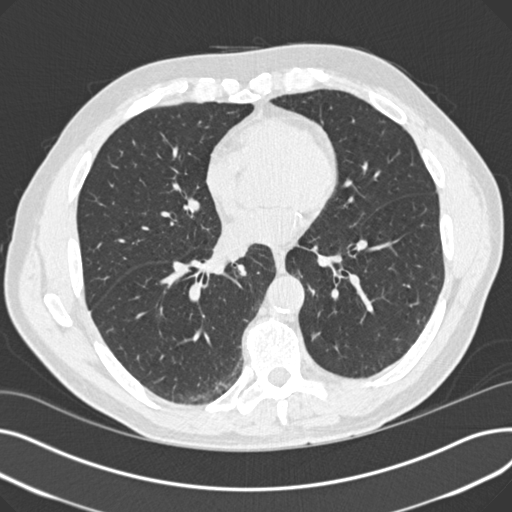
Low-dose screening chest CT, axial slice; second annual screen; lung window (W 1500 / L -600 HU); 2 mm slice thickness; standard (soft-tissue) reconstruction kernel (B30f); slice 96 of 163 in the series. Male, age 64 years at enrolment. Former smoker at enrolment.
Expert-annotated lung lesion, bounding box [x1, y1, x2, y2] px = [299, 317, 338, 362]. Screening reader's record for this exam (one nodule recorded; not confirmed to be the boxed lesion): non-calcified nodule or mass ≥4 mm, left lower lobe, 6 × 5 mm, smooth margins, ground glass attenuation, pre-existing on the prior screen: yes; interval growth: no. Official screen result: positive, no significant change: stable abnormalities potentially related to lung cancer, unchanged since the prior screening exam. Lung cancer was diagnosed 417 days after this screen: adenocarcinoma with mixed subtypes, left lower lobe, well differentiated (G1), stage IA (AJCC 6th edition), 7 mm at pathology.